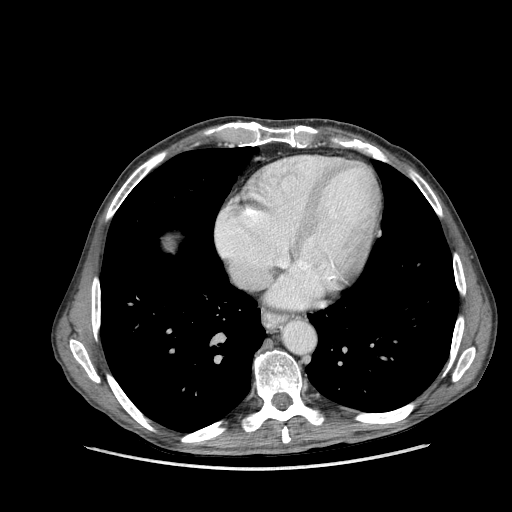
Contrast-enhanced abdominal CT (liver protocol), one axial slice; position 149 of 162 along the scan axis; 100 kVp; soft-tissue window (W 400 / L 40 HU); 512 × 512 image matrix, field of view 400 × 400 mm. Case-level facts recorded for this patient, not image findings: diagnosis: hepatocellular carcinoma (patient treated with transarterial chemoembolisation; whether this scan precedes or follows treatment is not stated here); TNM stage (as recorded): Stage-IIIA; Child-Pugh class: A; tumour nodularity: multinodular.
Outlined on this slice (semi-automatic segmentation, software-assisted and operator-edited):
- liver parenchyma outside the tumour (the mass and vessels are separate outlines, so this box may not span the whole liver): bounding box (x1, y1, x2, y2) in pixels: (164, 236, 174, 250)